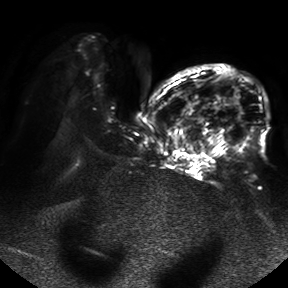
Breast MRI, one axial slice; diffusion-weighted series; image 2 of 4 stored at this slice position (different b-values; order by instance number); 1.5 T; 288 × 288 image matrix, field of view 390 × 390 mm. Female patient.
Outlined on this slice (manually delineated by an expert):
- tumour on diffusion-weighted imaging: bounding box (x1, y1, x2, y2) in pixels: (229, 96, 238, 106)